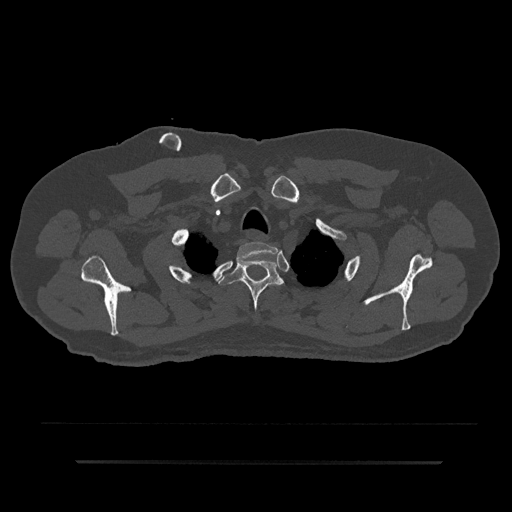
CT including the spine, one axial slice; position 705 of 797 along the scan axis; reconstruction kernel Br40s/3; bone window (W 1800 / L 400 HU); 0.5 mm slice thickness; 512 × 512 image matrix, field of view 464 × 464 mm. Male patient, age 59 years. From the clinical record (not read from this slice): primary cancer: bile ducts; vertebrae with lytic lesions (as recorded): T10.
Annotated regions visible in this slice (semi-automatically segmented with operator editing):
- T1 vertebra: box from (x=236, y=242) to (x=278, y=263) px
- T2 vertebra: (x=218, y=255)–(x=285, y=315)